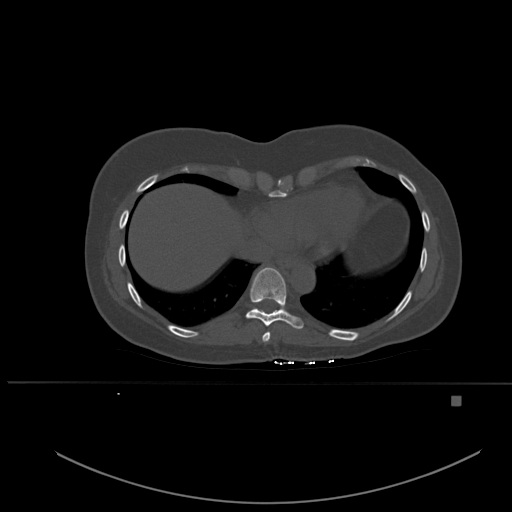
CT including the spine, one axial slice; position 305 of 651 along the scan axis; bone window (W 1800 / L 400 HU); 1.5 mm slice thickness; 512 × 512 image matrix, field of view 443 × 443 mm. Patient: female, 49 years. From the clinical record (not read from this slice): primary cancer: breast; vertebrae with lytic lesions (as recorded): L3, T12, L4.
Structures marked on this image (semi-automatically segmented with operator editing):
- T10 vertebra: bounding box (x1, y1, x2, y2) in pixels: (254, 308, 258, 310)
- T8 vertebra: (262, 332, 270, 342)
- T9 vertebra: (246, 267, 304, 333)